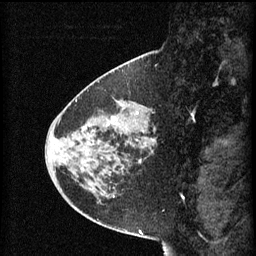
Breast MRI (dynamic contrast-enhanced), one sagittal slice; position 23 of 60 along the scan axis; 3 images stored at this slice position (order not interpretable as contrast timing); 1.5 T; TE 4.2 ms, TR 8.2 ms; 2 mm slice thickness; 256 × 256 image matrix. Patient: female, 45 years.
Outlined on this slice (semi-automatically segmented with operator editing):
- analysis volume of interest (the breast-tissue region the enhancement analysis was run in; not a lesion): box from (x=80, y=102) to (x=156, y=171) px
- tumour enhancement mask (voxels above the 70 % enhancement threshold inside the analysis volume of interest): (x=114, y=118)–(x=152, y=163)